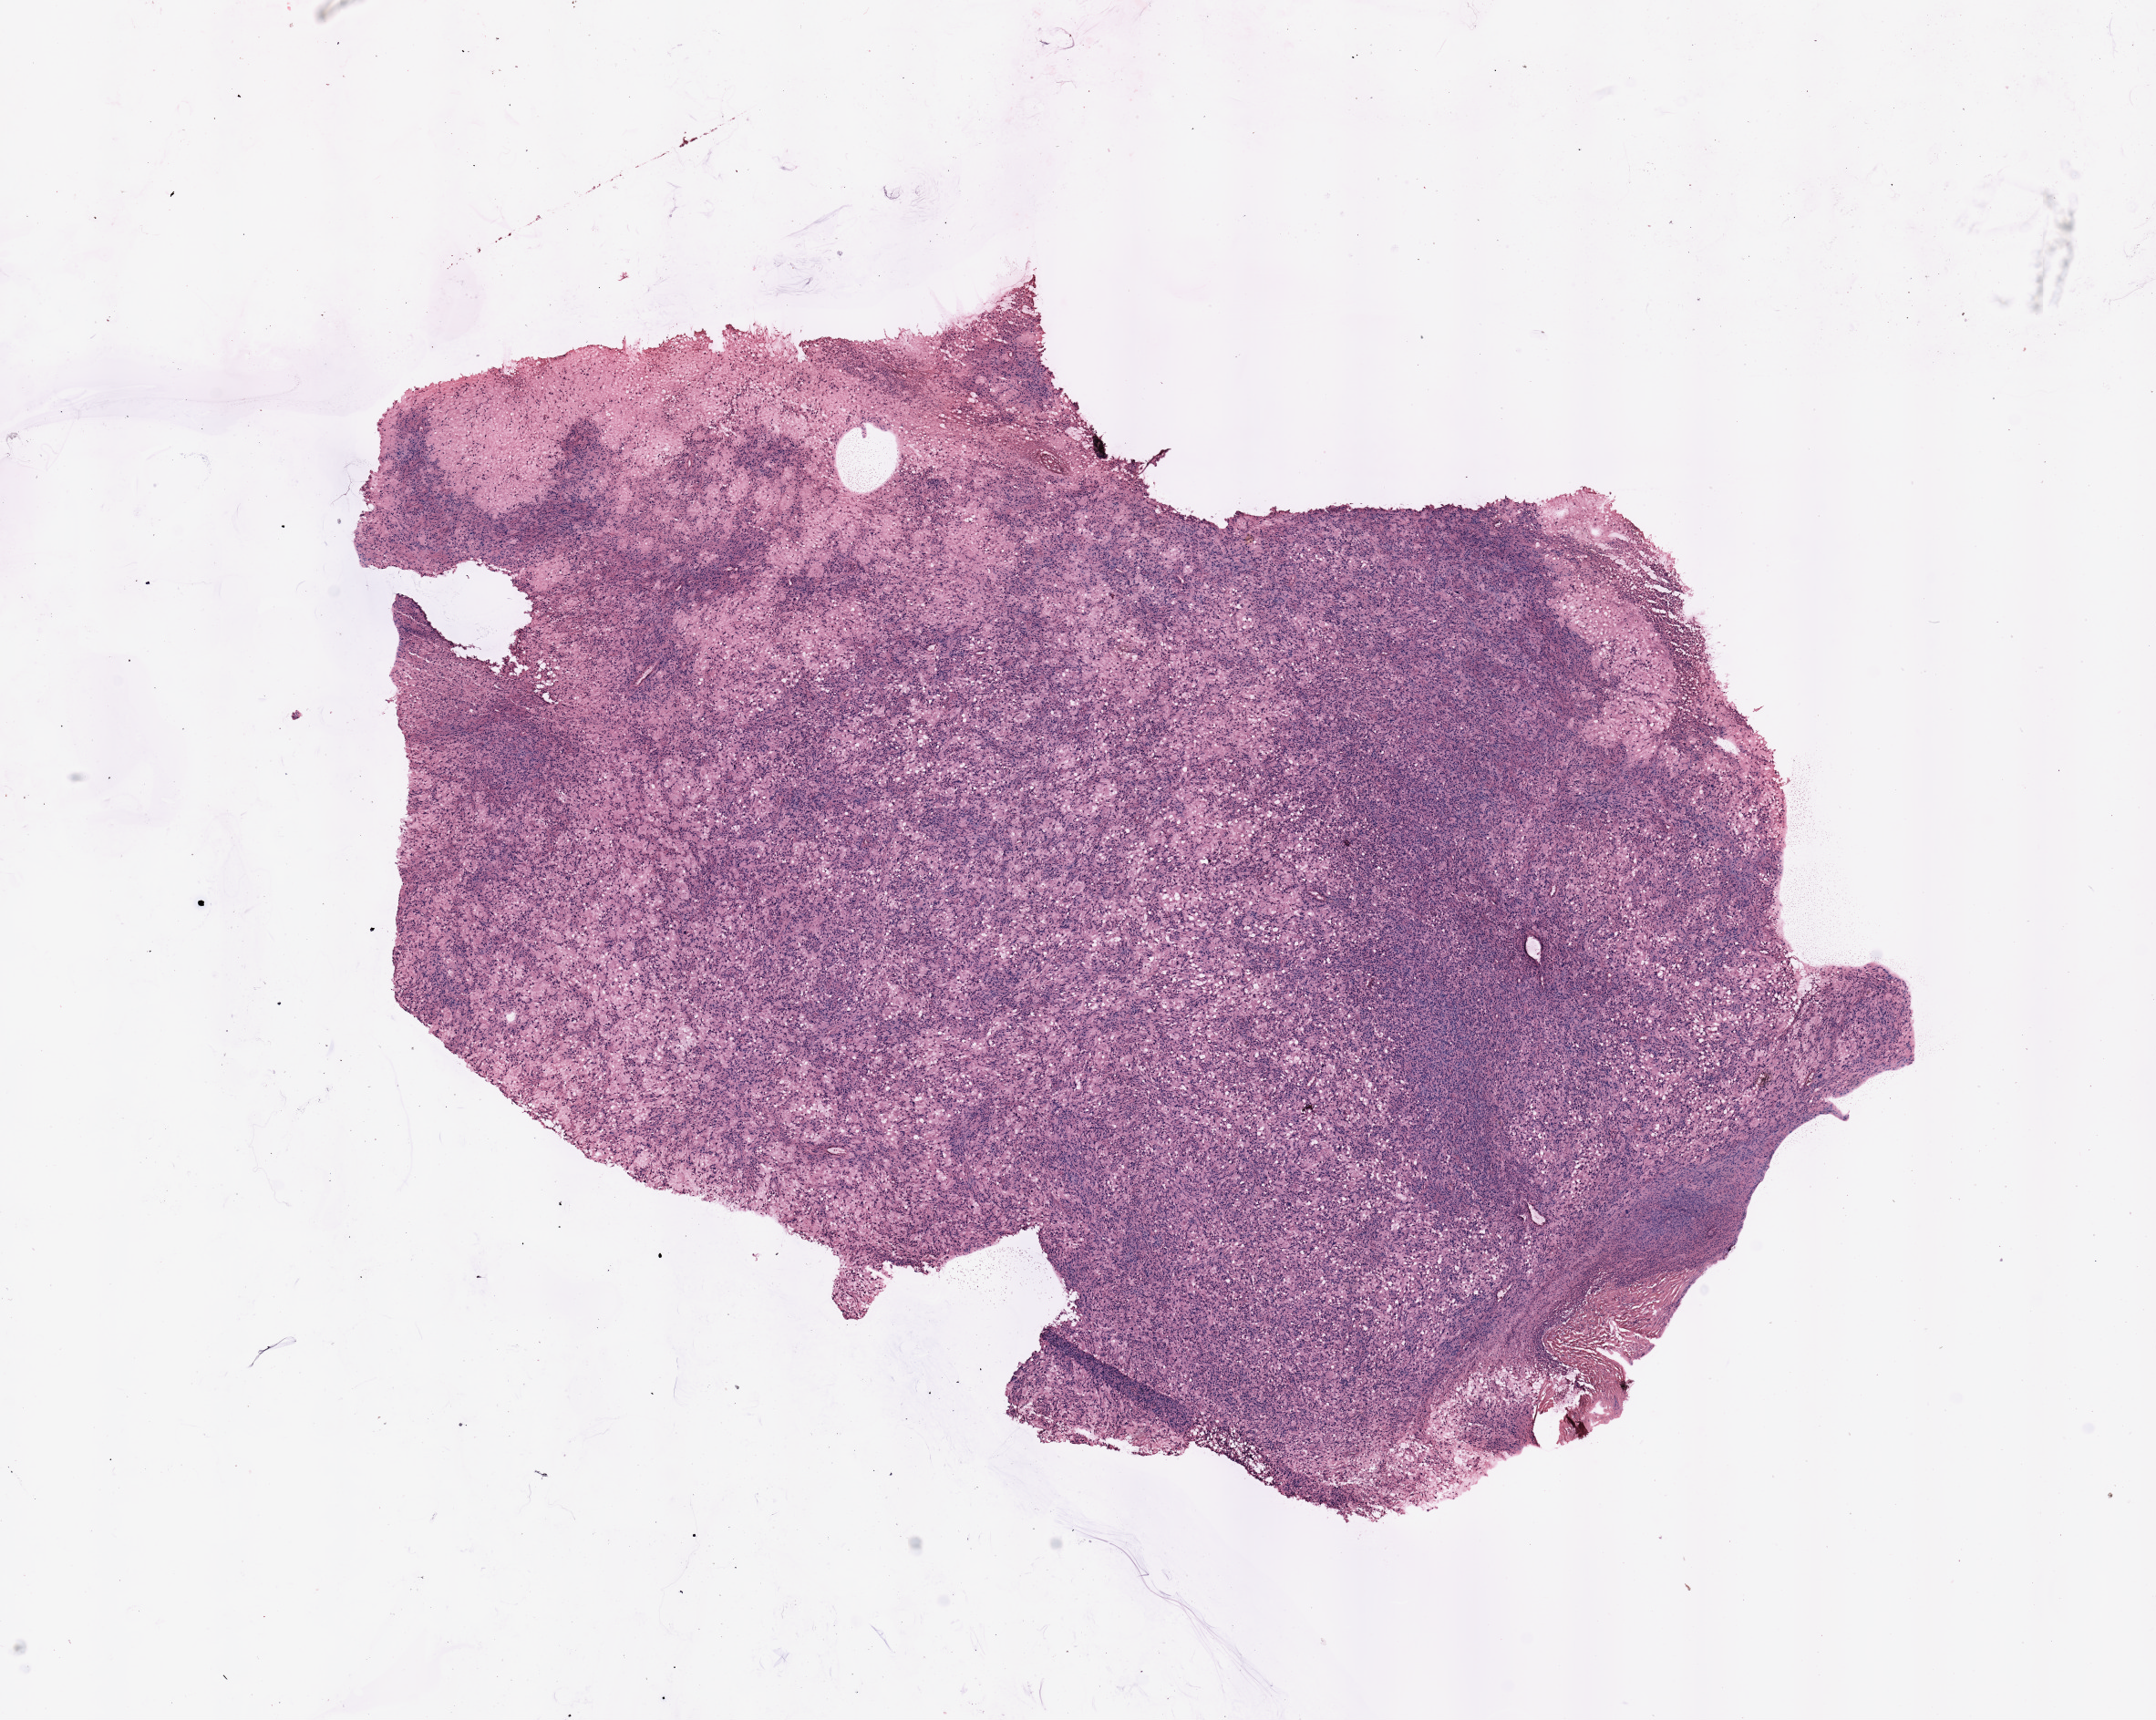
Whole-slide histology image, H&E-stained, shown as a low-resolution overview of the whole scanned area (about 18.7 x 14.9 mm, acquisition: 20x scan); tumour tissue sample. Patient: male, age 74 years.
• primary tumour site (as recorded): lower extremity
• patient diagnosis (cohort enrolment): sarcoma (site not recorded at cohort level)